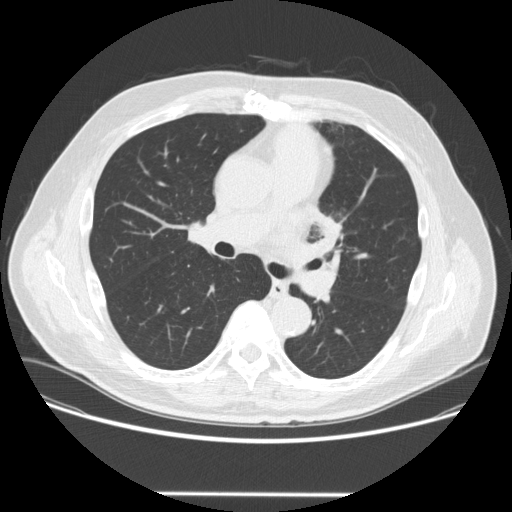
Chest CT (low-dose screening protocol), one axial image. Third annual screen. Lung window (W 1500 / L -600 HU). 2.5 mm slice thickness. Standard (soft-tissue) reconstruction kernel (STANDARD). Male, age 66 years at enrolment. Former smoker at enrolment.
Lesion marked by an expert reader, bounding box [x1, y1, x2, y2] px = [301, 209, 353, 256]. The screening reader recorded 2 non-calcified nodules or masses ≥4 mm on this exam; which of them this box marks is not recorded.